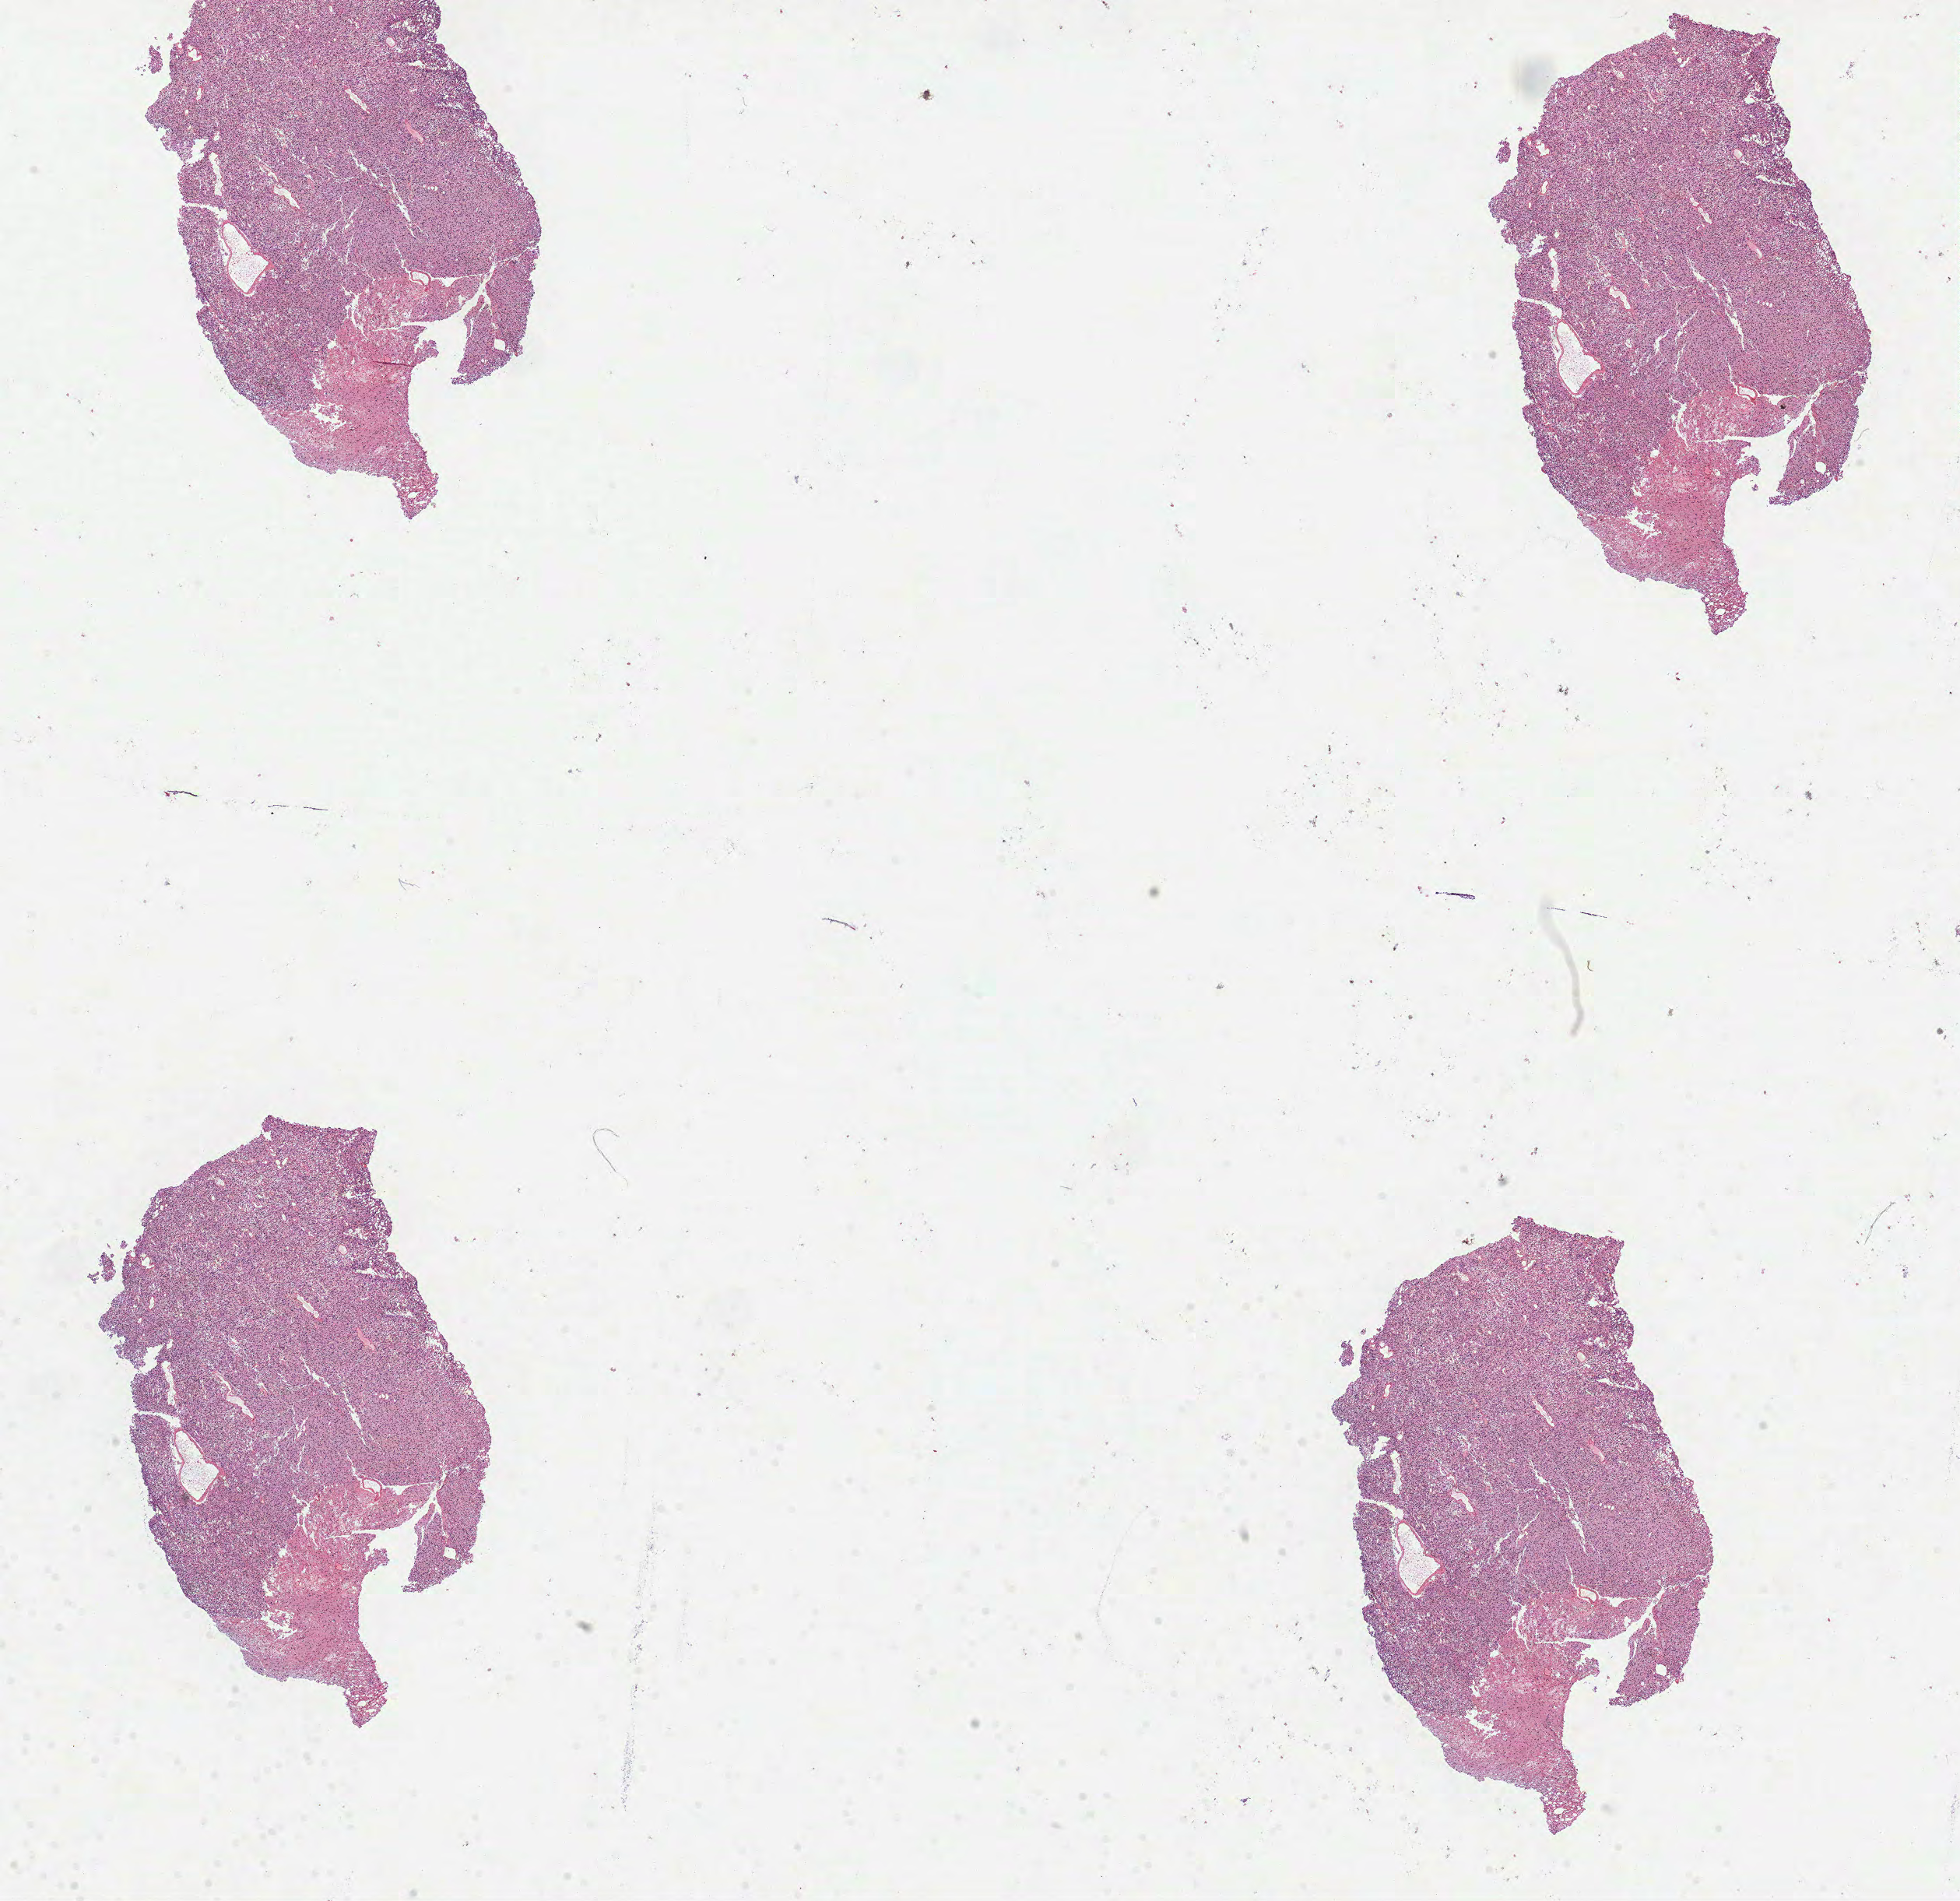
Digitized Hematoxylin and eosin (H&E) stained tissue section (whole slide) — a low-resolution overview of the entire scanned area, about 20.3 x 19.7 mm; FFPE section; primary tumour sample from the brain. Female, age 31 years at initial diagnosis. Histologic grade: G2 (moderately differentiated).
Histologic diagnosis: Oligodendroglioma, NOS (cerebrum). Laterality: left.